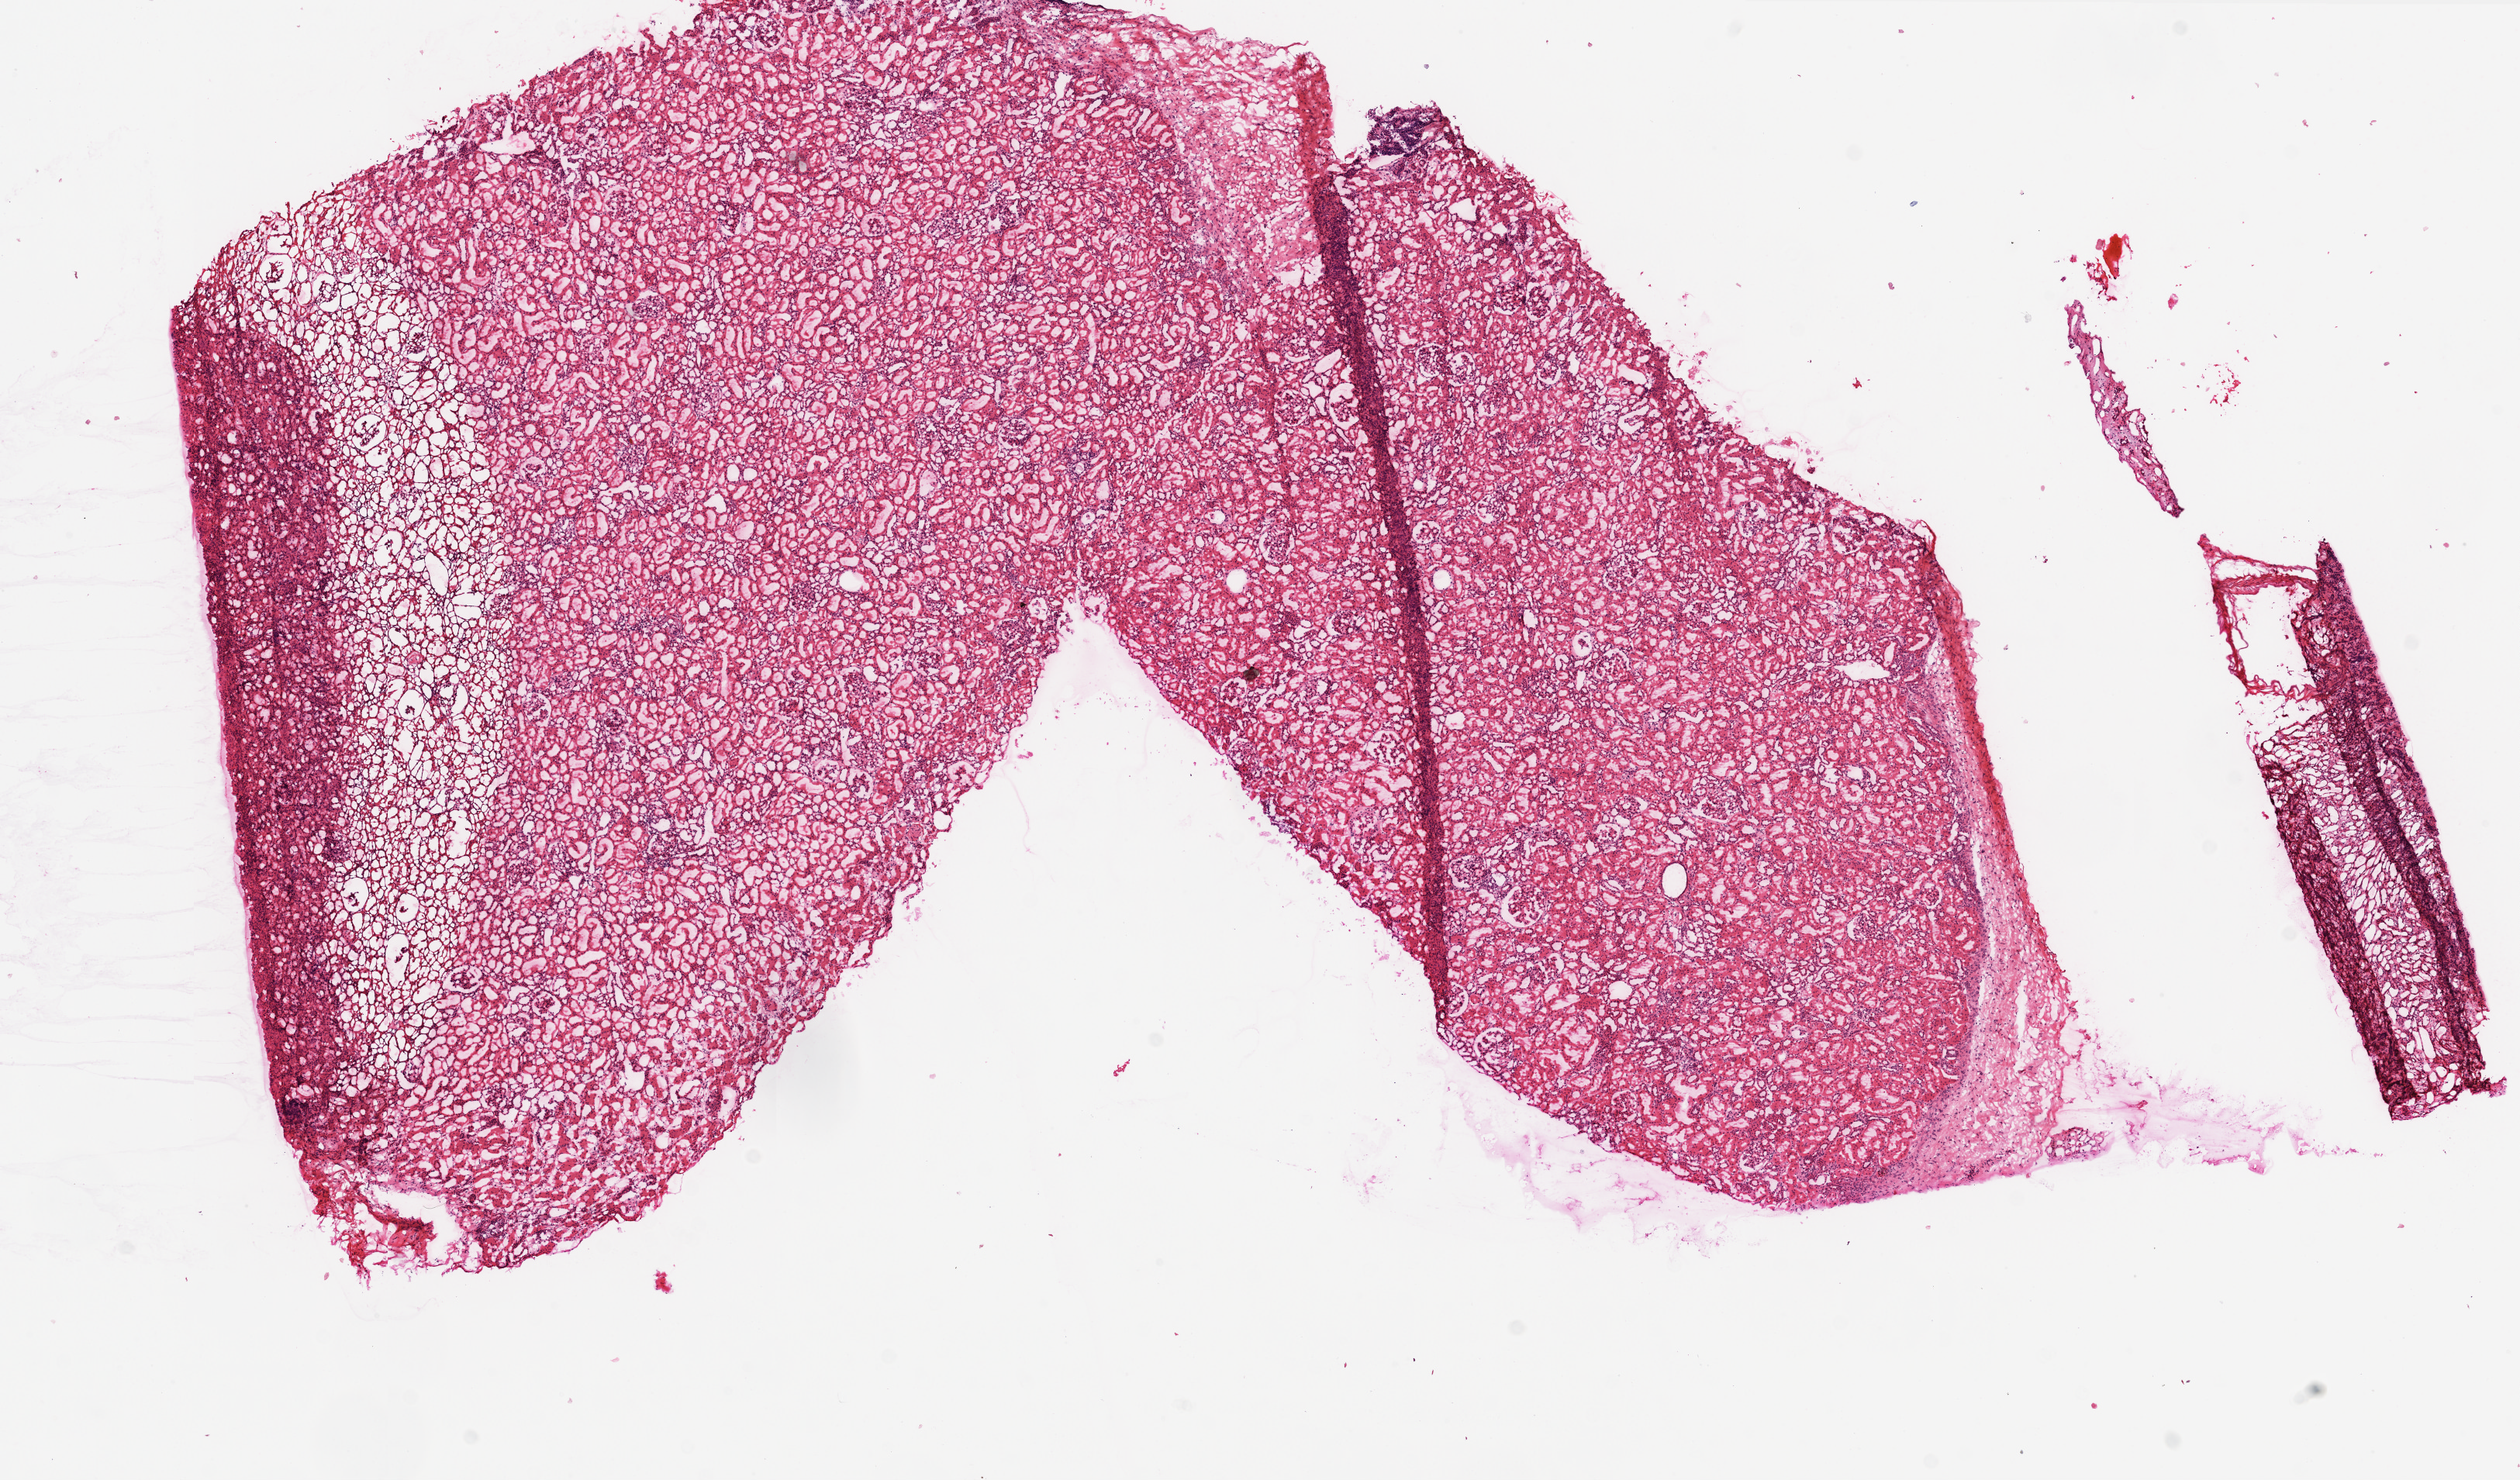
H&E-stained whole-slide image — shown as a low-resolution overview of the whole scanned area (about 13.0 x 7.7 mm, from a 20x scan); frozen section from the top of the tissue portion; sample: solid tissue normal (non-tumour tissue), kidney. Female, age 60 years at initial diagnosis.
This section: solid tissue normal (non-tumour) sample from the same patient. Patient diagnosis: Clear cell adenocarcinoma, NOS.